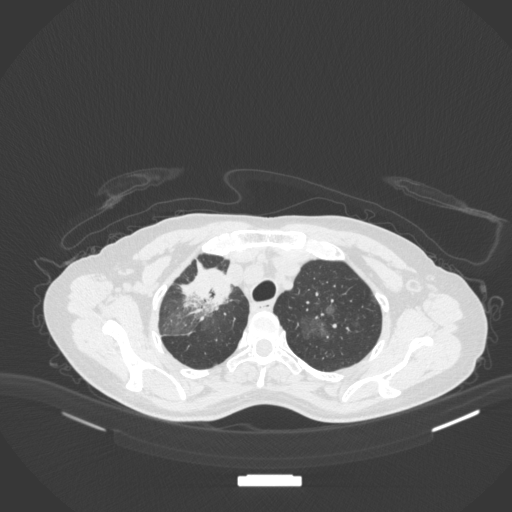
Chest CT, one axial slice; slice 266 of 311 in the series (ordered by position); lung window (W 1500 / L -600 HU); 512 × 512 image matrix, field of view 400 × 400 mm. Patient: female, 59 years. Case-level facts recorded for this patient, not image findings: clinical TNM (as recorded): T3 N0 M0; histopathological grade: G1.
Structures marked on this image (bounding box drawn by a radiologist):
- lung tumour (recorded histology: adenocarcinoma): bounding box <178,257,238,323> (left, top, right, bottom; pixels)